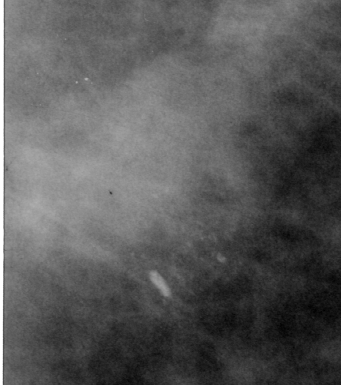
Region of interest cut from a scanned film mammogram (one marked finding); left breast; MLO view.
- Calcifications, morphology pleomorphic, distribution clustered; BI-RADS assessment category 4; pathology result (as recorded, not read from the image): malignant.